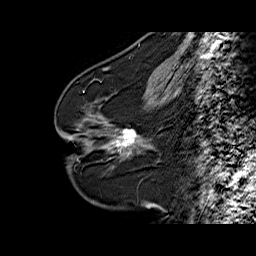
Breast MRI (dynamic contrast-enhanced), one sagittal slice; slice 27 of 60 in the series (ordered by position); dynamic contrast-enhanced series, time point 2 of 6 at this slice position (early post-contrast); 1.5 T; TE 6.3 ms, TR 32.5 ms; 256 × 256 image matrix, field of view 200 × 200 mm. Female patient. From the clinical record (not read from this slice): setting: breast cancer imaged before/during neoadjuvant chemotherapy; receptor status: HR-positive, HER2-negative.
Outlined on this slice (semi-automatically segmented with operator editing):
- analysis volume of interest (the breast-tissue region the enhancement analysis was run in; not a lesion): bounding box <94,103,161,163> (left, top, right, bottom; pixels)
- tumour enhancement mask (voxels above the 100 % enhancement threshold inside the analysis volume of interest): <111,130,137,147>